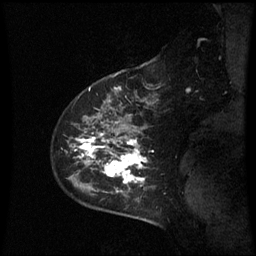
Breast MRI (dynamic contrast-enhanced), one sagittal slice; slice 47 of 60 in the series (ordered by position); dynamic contrast-enhanced series, image 2 of 3 at this slice position (ordered by acquisition); 1.5 T; TE 4.2 ms, TR 8.9 ms; 256 × 256 image matrix. Female patient, age 43 years. From the clinical record (not read from this slice): setting: breast cancer imaged before/during neoadjuvant chemotherapy; receptor status: HER2-positive.
Structures marked on this image (semi-automatically segmented with operator editing):
- analysis volume of interest (the breast-tissue region the enhancement analysis was run in; not a lesion): bounding box [x1, y1, x2, y2] px = [56, 80, 160, 195]
- tumour enhancement mask (voxels above the 70 % enhancement threshold inside the analysis volume of interest): [77, 134, 148, 185]